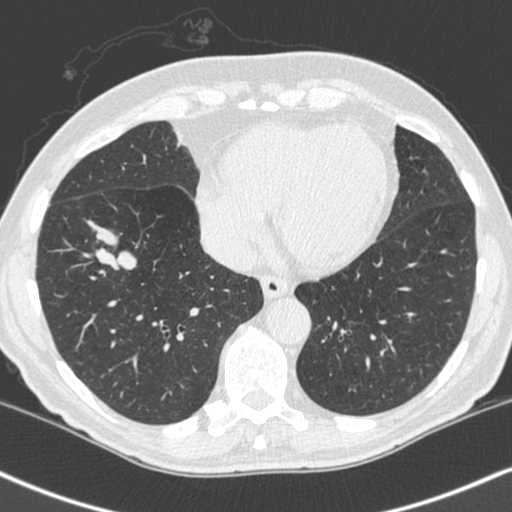
Low-dose screening chest CT, axial slice. Baseline annual screen. Lung window (W 1500 / L -600 HU). Standard (soft-tissue) reconstruction kernel (C). Slice 159 of 248 in the series. Male, age 68 years at enrolment.
Lesion marked by an expert reader, box from (x=78, y=203) to (x=153, y=272) px. Reader record for this screening exam (exam-level; its link to the box is not recorded): non-calcified nodule or mass ≥4 mm, right lower lobe, 34 × 17 mm, smooth margins, soft tissue attenuation. Participant outcome: lung cancer diagnosed 24 days after this screen — combined small cell carcinoma, right lower lobe, stage IIIA (AJCC 6th edition), 41 mm at pathology.